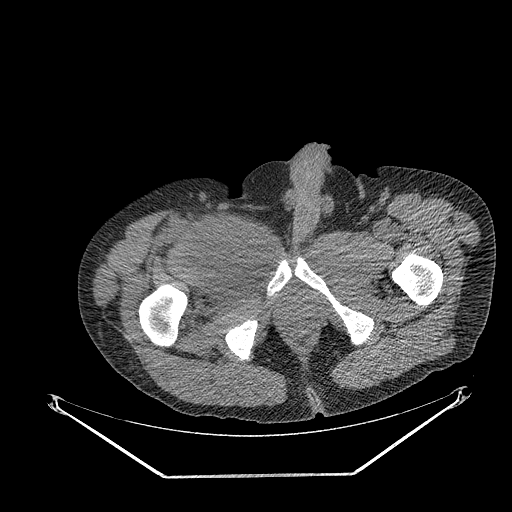
CT of an extremity soft-tissue mass (from a PET/CT study), one axial slice. Position 290 of 311 along the scan axis. Reconstruction kernel STANDARD. 140 kVp. Soft-tissue window (W 400 / L 40 HU). 512 × 512 image matrix, field of view 500 × 500 mm. Male patient. Case-level facts recorded for this patient, not image findings: histological type: undifferentiated - pleiomorphic; grade: high; site of the primary tumour: right thigh.
Structures marked on this image (expert contour drawn on MRI and transferred to this co-registered scan by the dataset authors):
- gross tumour volume including surrounding oedema: bounding box [x1, y1, x2, y2] px = [212, 215, 252, 245]
- gross tumour volume (mass): [215, 226, 238, 243]